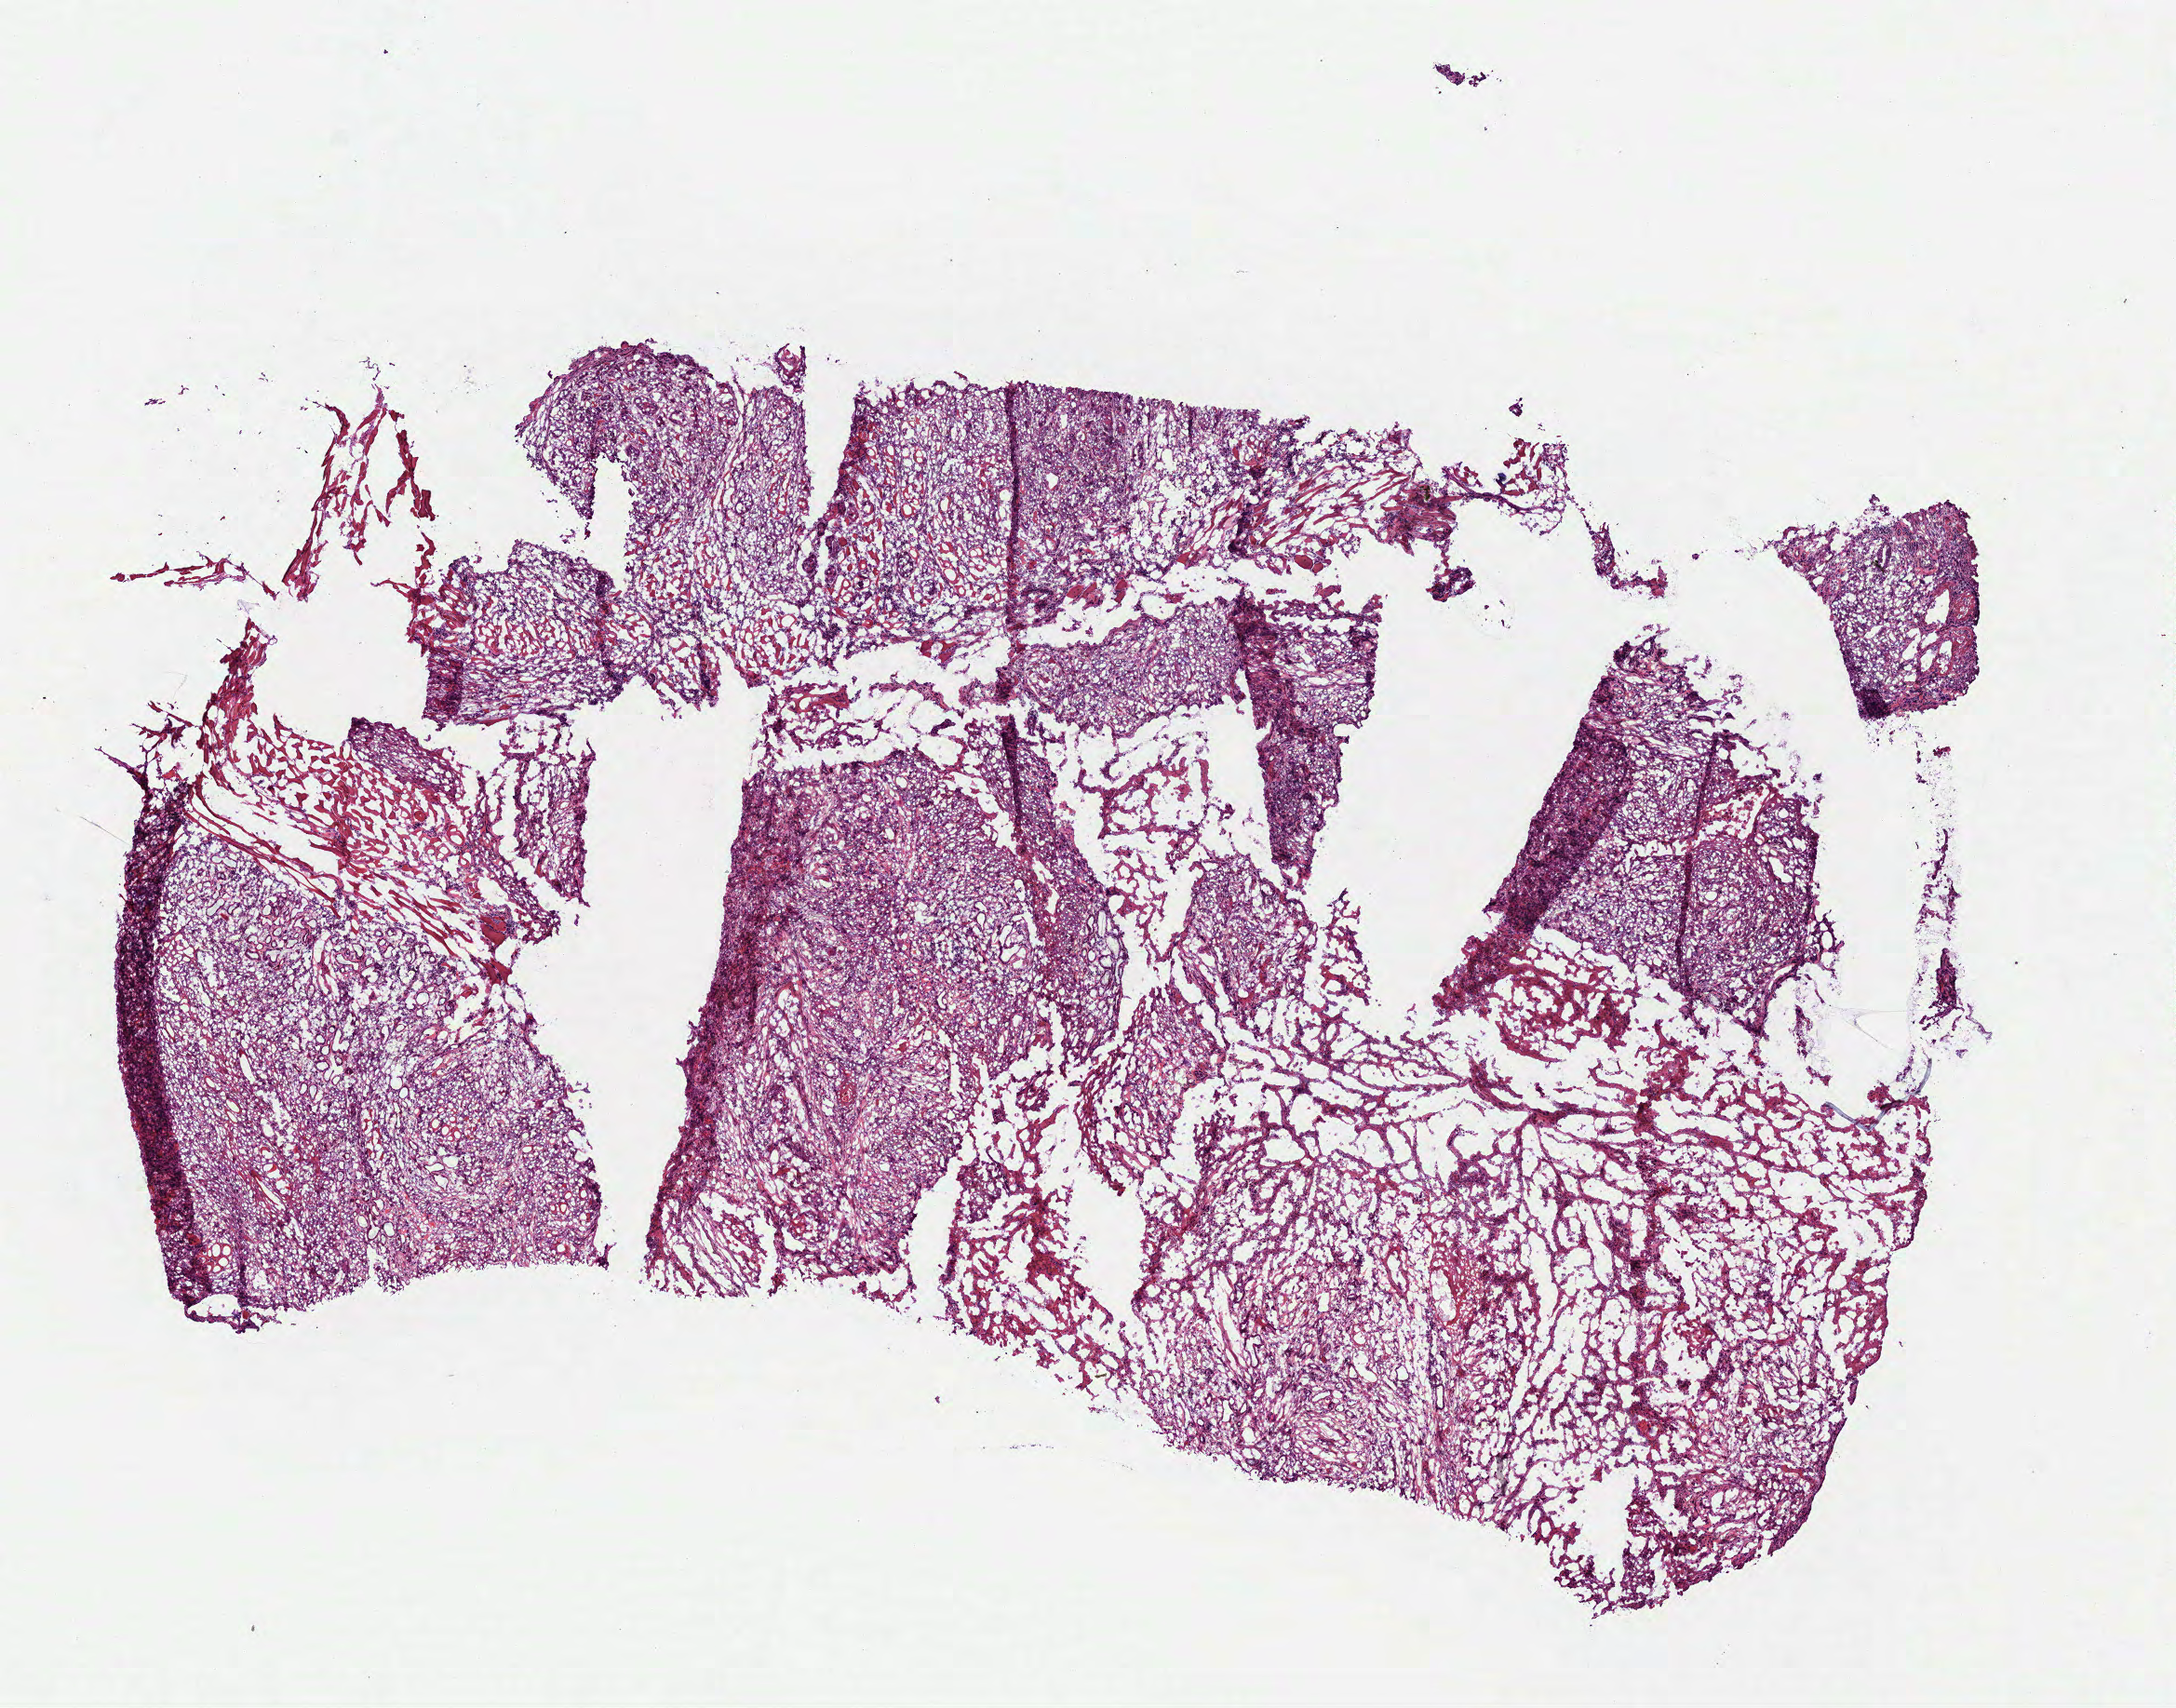
Whole-slide histology image, H&E-stained — whole scanned area (about 9.4 x 7.4 mm) shown as a low-resolution overview, frozen section from the bottom of the tissue portion, sample: primary tumour, head and neck. Patient: male, age at initial diagnosis 64 years. Histologic grade: G2 (moderately differentiated). Composition of this section per pathologist review: tumour cells 90%, tumour nuclei 80%, normal cells 9%, stromal cells 0%, necrosis 1%. Inflammatory infiltration, as recorded: lymphocyte infiltration 10%, monocyte infiltration 0%, neutrophil infiltration 5%.
AJCC pathologic stage: IVA. TNM: T3 N2c. Pathologic diagnosis: Squamous cell carcinoma, NOS (base of tongue, NOS).